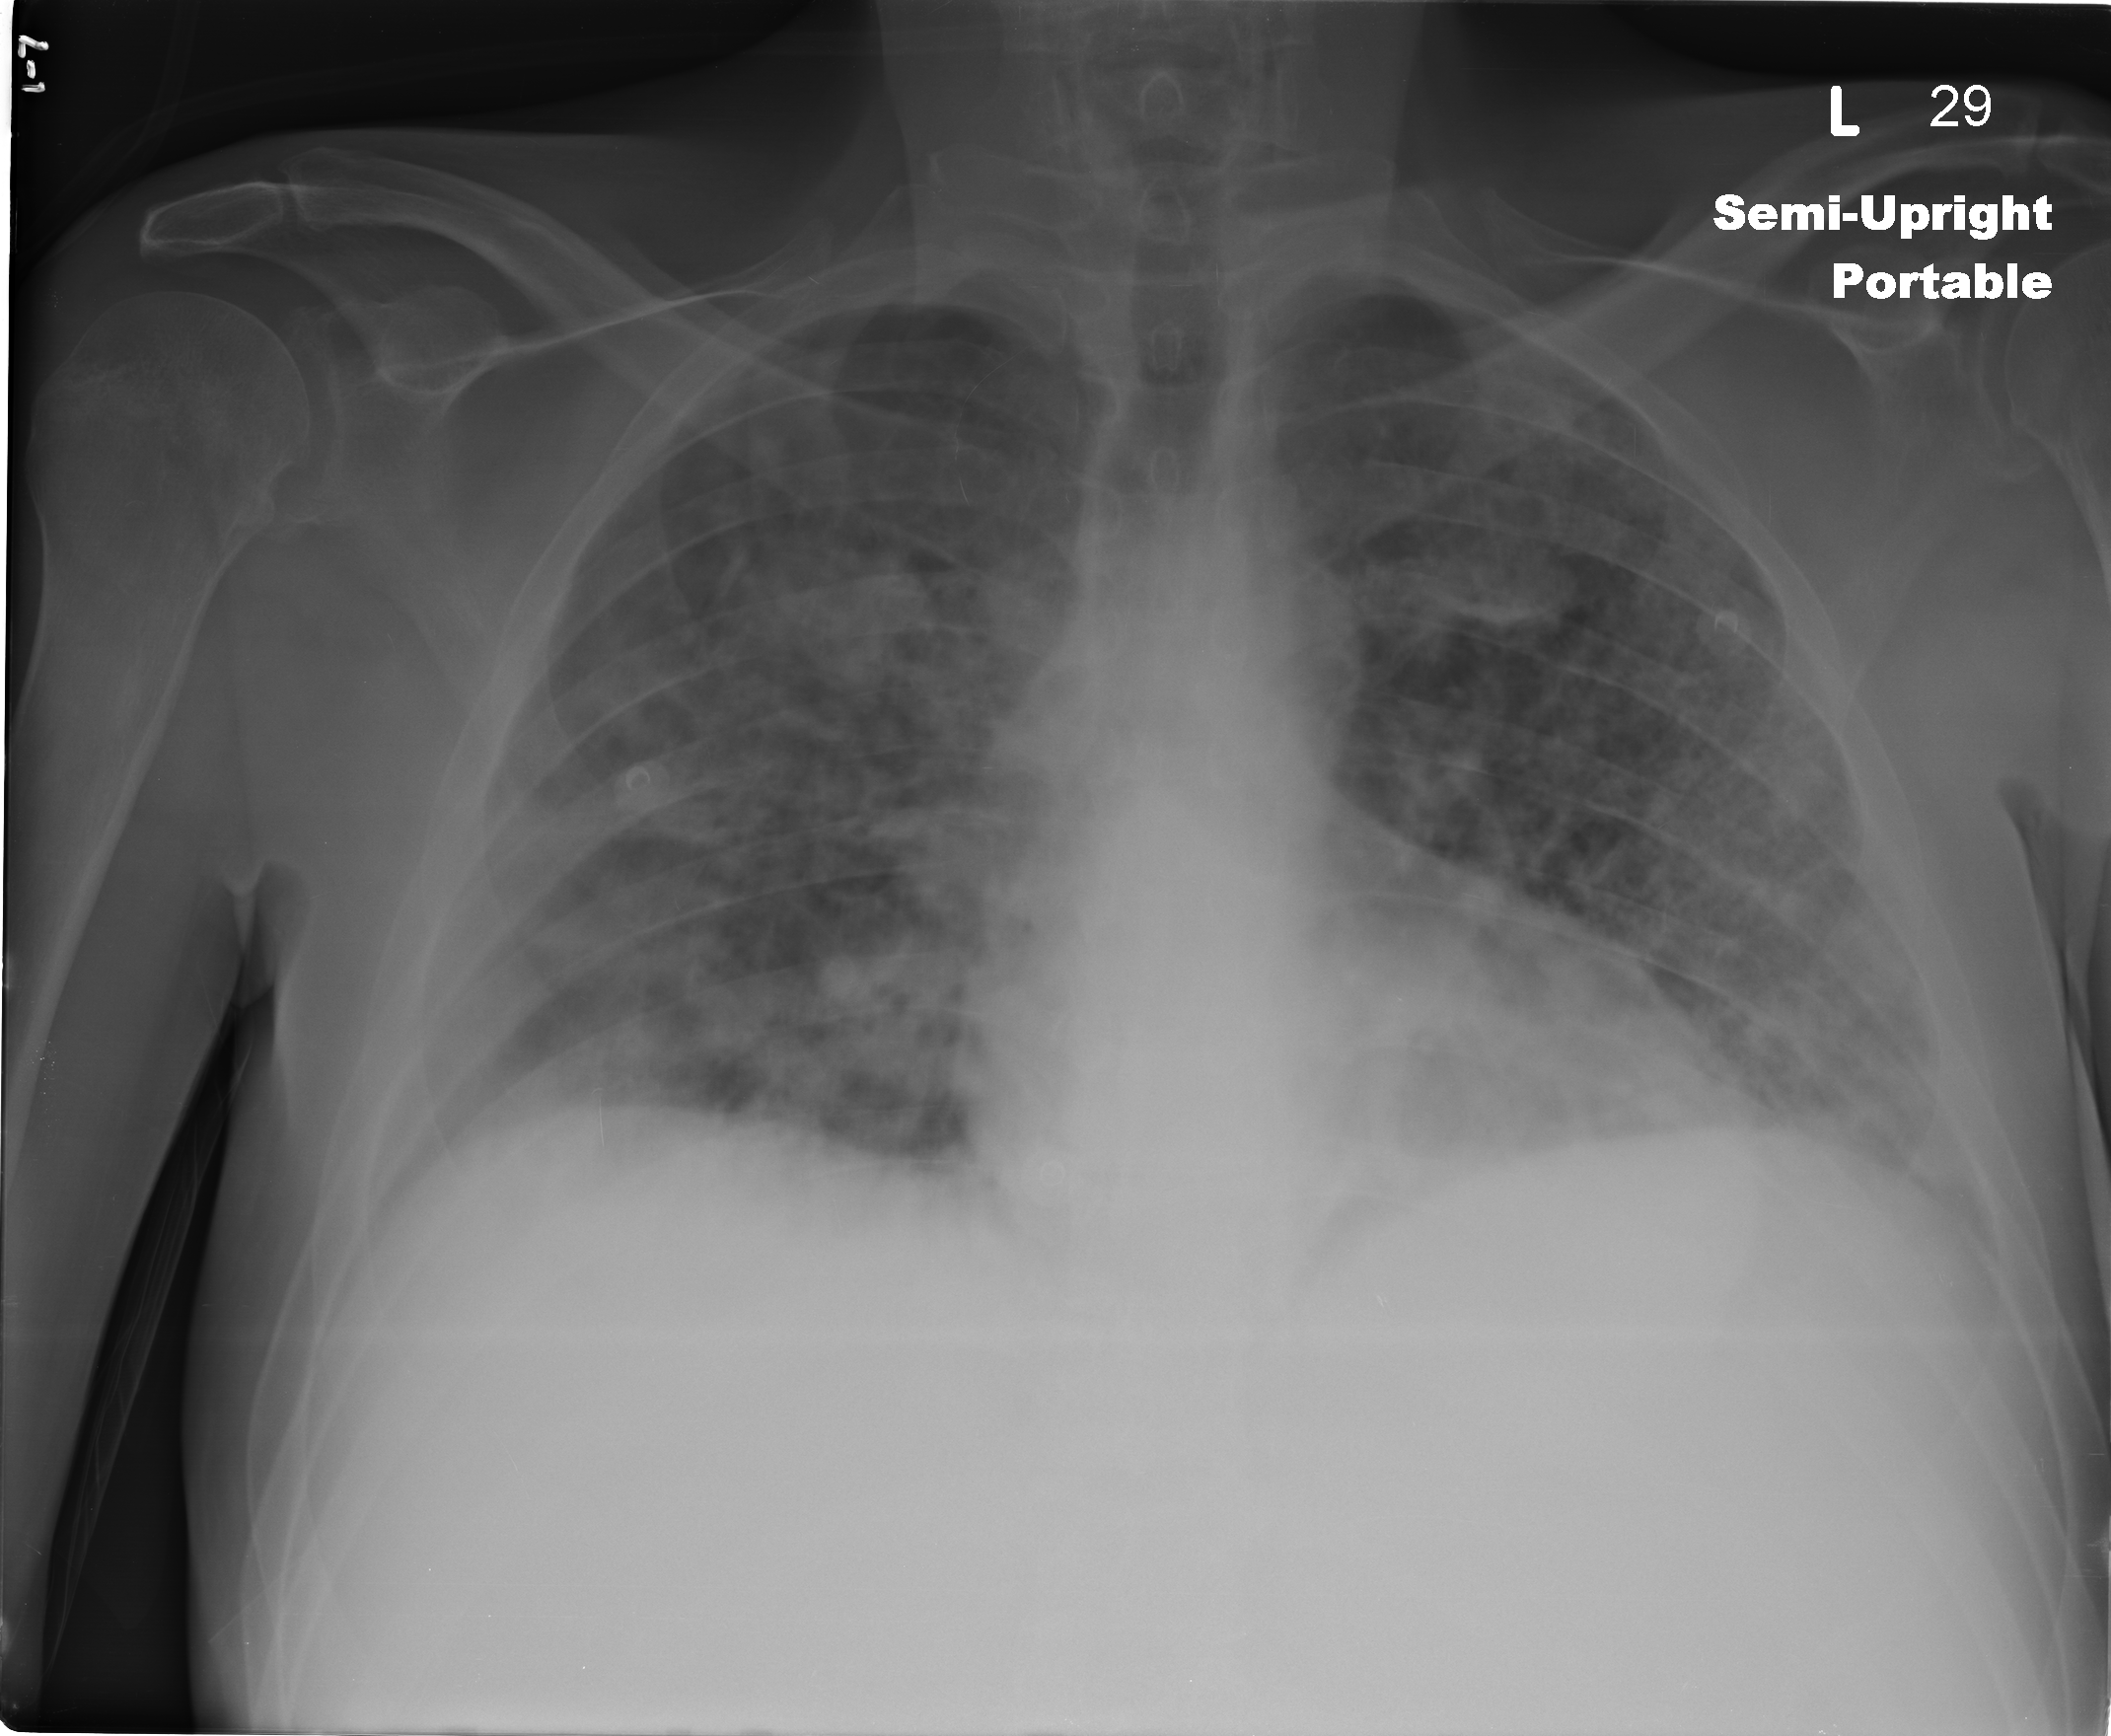
Chest X-ray (portable), AP projection. Male patient, age 54 years; imaged 0 days after the COVID-19 diagnosis.
Radiologist's key findings for this exam: Chronic lung disease/emphysema noted. Multifocal airspace opacities are noted throughout both lungs.